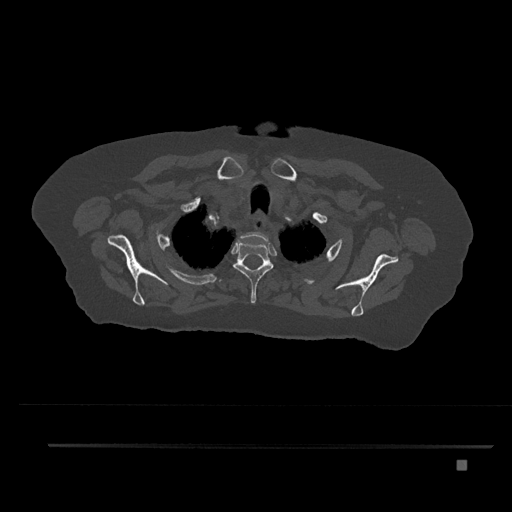
CT including the spine, one axial slice. Slice 668 of 797 in the series (ordered by position). Reconstruction kernel Br40s/3. 120 kVp. Bone window (W 1800 / L 400 HU). 0.5 mm slice thickness. 512 × 512 image matrix. Patient: female, 76 years. Case-level facts recorded for this patient, not image findings: primary cancer: lung; vertebrae with lytic lesions (as recorded): T11, L3.
Outlined on this slice (semi-automatically segmented with operator editing):
- T1 vertebra: box from (x=240, y=232) to (x=269, y=248) px
- T2 vertebra: (x=233, y=240)–(x=274, y=303)